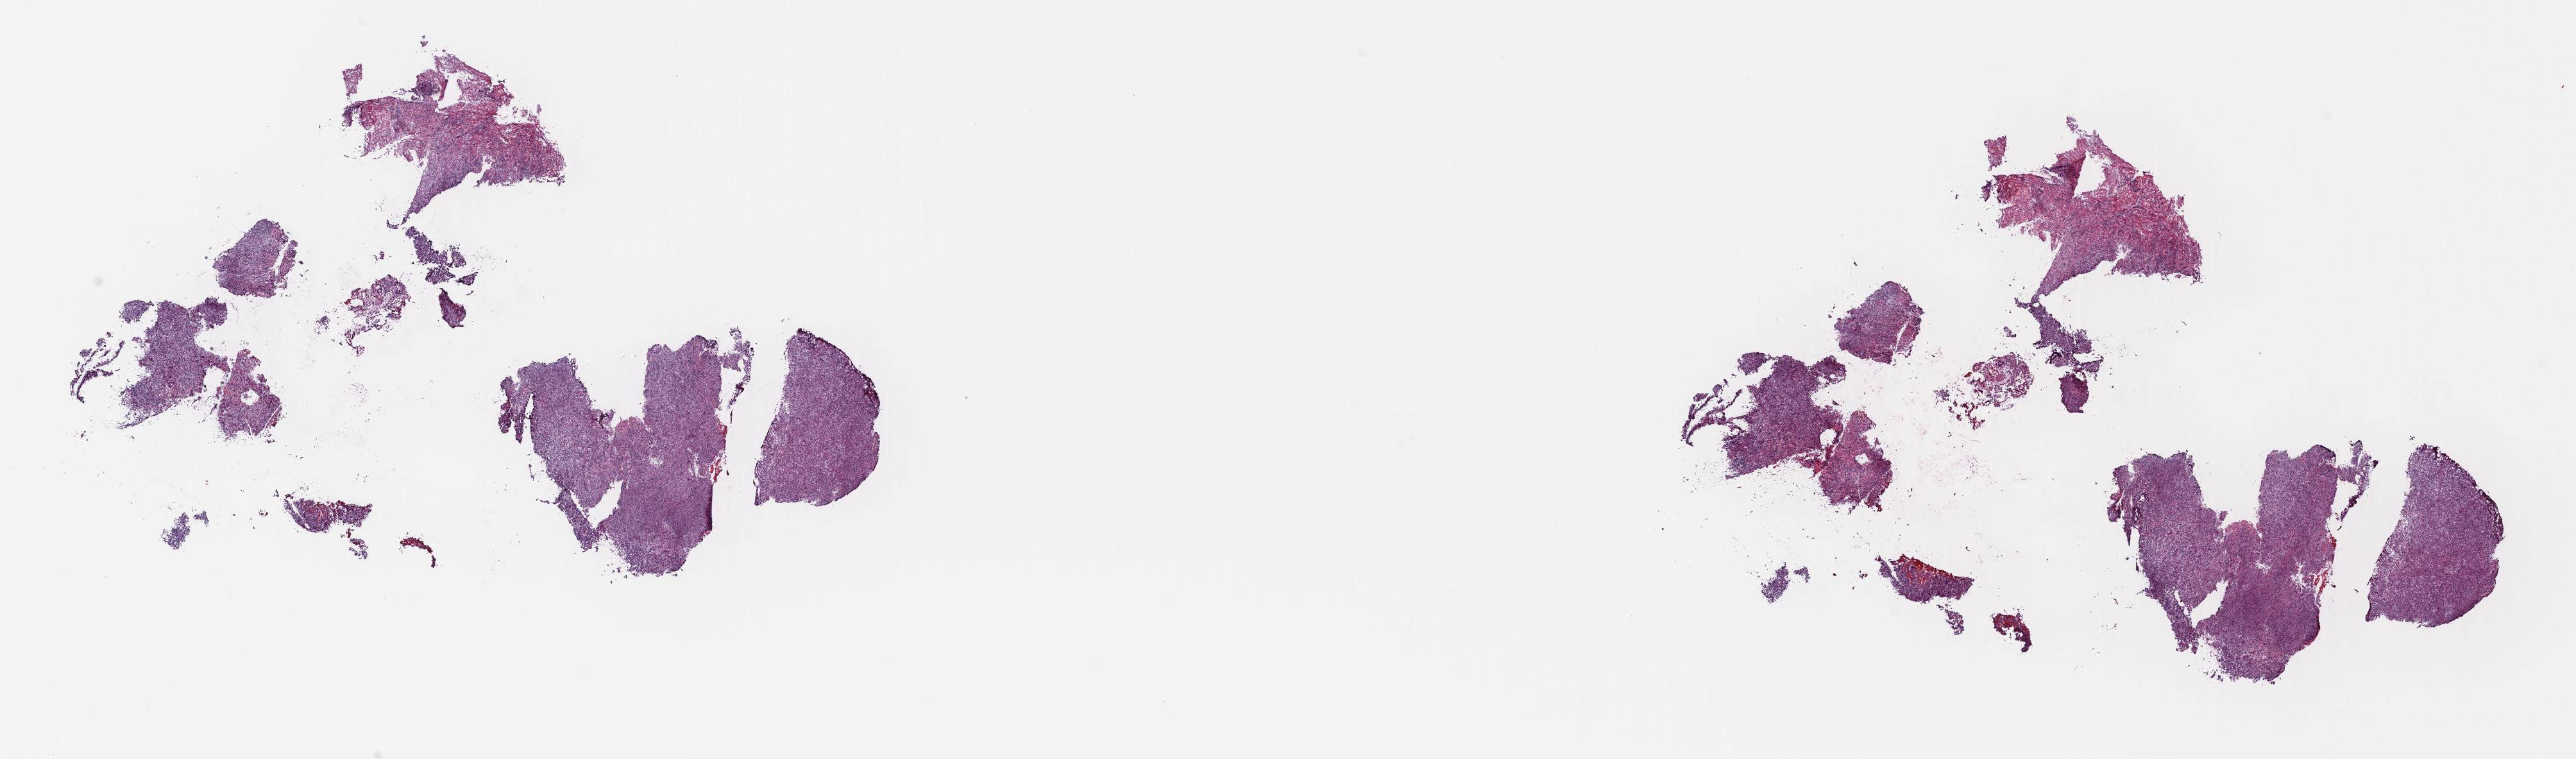
H&E whole-slide image, shown as a low-resolution overview of the whole scanned area (about 31.6 x 9.3 mm), frozen section from the top of the tissue portion, primary tumour sample from the mesothelium. Male, age 58 years at initial diagnosis. Pathologist review of this section (percent, as recorded): tumour cells 85%, tumour nuclei 100%, normal cells 0%, stromal cells 15%, necrosis 0%. Inflammatory infiltration, as recorded: lymphocyte infiltration 5%, monocyte infiltration 0%, neutrophil infiltration 0%.
- TNM: T2 N0 M0
- histologic diagnosis: Mesothelioma, biphasic, malignant (pleura, NOS)
- AJCC pathologic stage: II (7th edition)